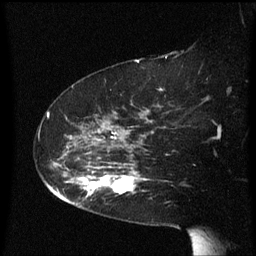
Breast MRI (dynamic contrast-enhanced), one sagittal slice. Dynamic contrast-enhanced series, image 2 of 3 at this slice position (ordered by acquisition). 1.5 T. TE 4.2 ms, TR 8.4 ms. 2.3 mm slice thickness. 256 × 256 image matrix, field of view 200 × 200 mm. Patient: female, 63 years. Case-level facts recorded for this patient, not image findings: setting: breast cancer imaged before/during neoadjuvant chemotherapy; receptor status: HER2-positive.
Annotated regions visible in this slice (semi-automatically segmented with operator editing):
- analysis volume of interest (the breast-tissue region the enhancement analysis was run in; not a lesion): bounding box <71,144,147,207> (left, top, right, bottom; pixels)
- tumour enhancement mask (voxels above the 70 % enhancement threshold inside the analysis volume of interest): <80,176,136,197>